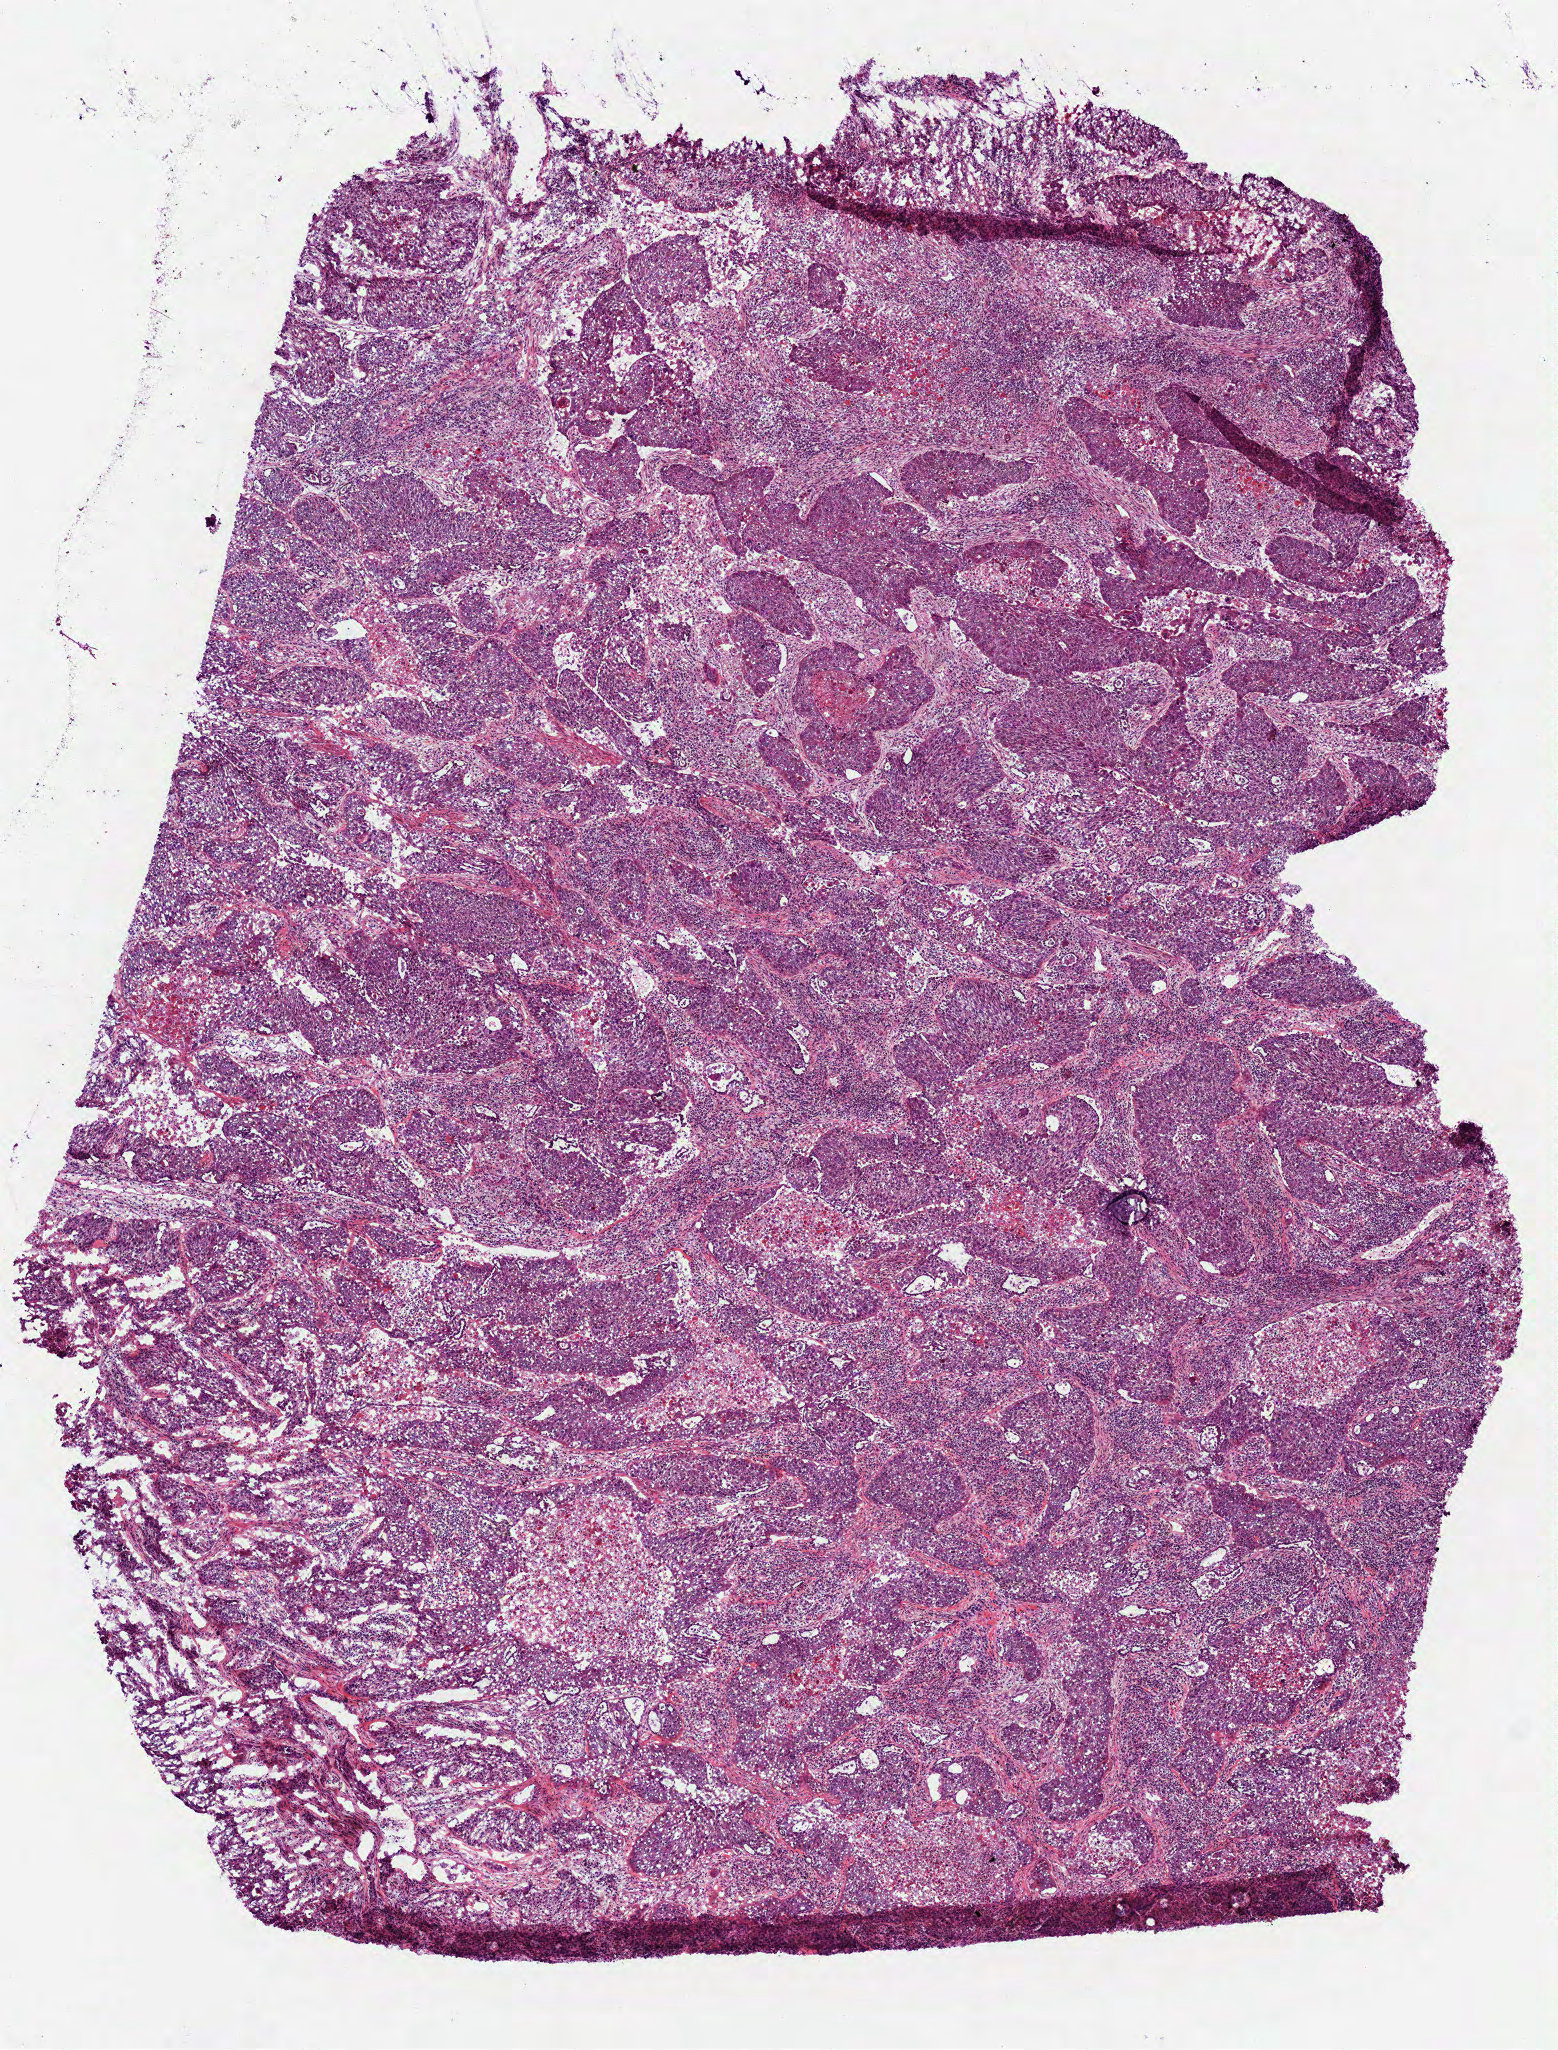
Digitized Hematoxylin and eosin (H&E) stained tissue section (whole slide), a low-resolution overview of the entire scanned area, about 6.3 x 8.3 mm (from a 40x scan), frozen section from the bottom of the tissue portion, lung, primary tumour sample. Patient: male, age at initial diagnosis 75 years. Composition of this section per pathologist review: tumour cells 100%, tumour nuclei 55%, normal cells 0%, stromal cells 0%, necrosis 0%. Inflammatory infiltration, as recorded: lymphocyte infiltration 20%, monocyte infiltration 0%, neutrophil infiltration 15%.
Diagnosis: Squamous cell carcinoma, NOS (upper lobe, lung). AJCC pathologic stage: IB (6th edition).